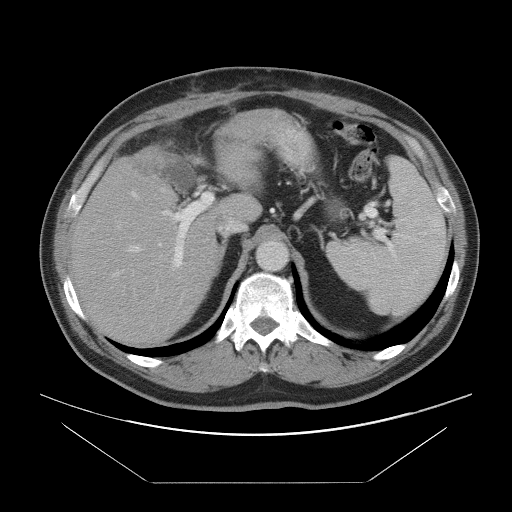
Contrast-enhanced abdominal CT, one axial slice. Position 60 of 97 along the scan axis. 120 kVp. Intravenous contrast given. Soft-tissue window (W 400 / L 40 HU). 5 mm slice thickness. 512 × 512 image matrix, field of view 442 × 442 mm. Male patient, age 62 years. Case-level facts recorded for this patient, not image findings: diagnosis: colorectal cancer liver metastases, imaged before liver resection; multiple liver metastases: no; largest metastasis: 7 cm; disease in both lobes: yes.
Structures marked on this image (manually delineated by an expert):
- hepatic veins: box from (x=129, y=188) to (x=167, y=252) px
- liver: (x=74, y=113)–(x=279, y=344)
- planned liver remnant (the part of the liver to remain after resection): (x=74, y=175)–(x=229, y=344)
- portal vein (with intrahepatic branches): (x=131, y=192)–(x=214, y=272)
- liver metastasis: (x=130, y=153)–(x=161, y=179)